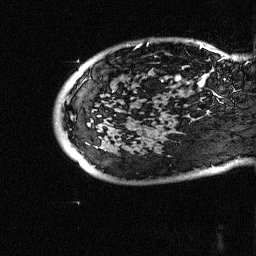
Breast MRI (dynamic contrast-enhanced), one sagittal slice; position 10 of 64 along the scan axis; dynamic contrast-enhanced study with each time point stored as its own series, time point 2 of 3 at this slice position (early post-contrast, ordered by acquisition time); 1.5 T; TE 4.5 ms, TR 11 ms; 2.5 mm slice thickness; 256 × 256 image matrix, field of view 200 × 200 mm. Patient: female, 38 years. From the clinical record (not read from this slice): setting: breast cancer imaged before/during neoadjuvant chemotherapy; receptor status: HR-positive, HER2-negative.
Structures marked on this image (semi-automatic segmentation, software-assisted and operator-edited):
- analysis volume of interest (the breast-tissue region the enhancement analysis was run in; not a lesion): bounding box [x1, y1, x2, y2] px = [88, 18, 252, 126]
- tumour enhancement mask (voxels above the 90 % enhancement threshold inside the analysis volume of interest): [174, 44, 209, 83]